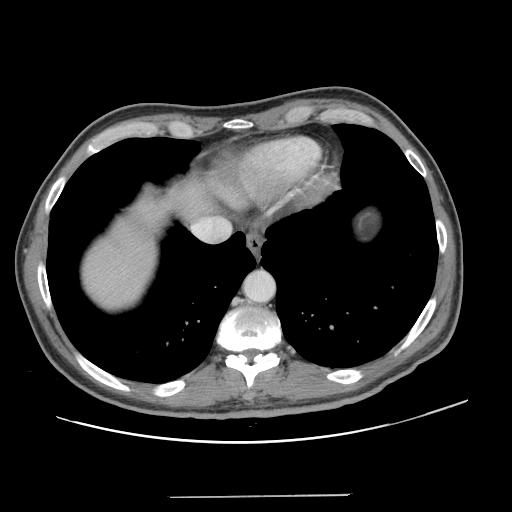
Contrast-enhanced abdominal CT, one axial slice. Slice 119 of 131 in the series (ordered by position). Intravenous contrast given. Soft-tissue window (W 400 / L 40 HU). 512 × 512 image matrix, field of view 403 × 403 mm. Male patient, age 60 years. From the clinical record (not read from this slice): diagnosis: colorectal cancer liver metastases, imaged before liver resection.
Structures marked on this image (outlined manually by an expert reader):
- liver: bounding box (x1, y1, x2, y2) in pixels: (82, 182, 211, 309)
- planned liver remnant (the part of the liver to remain after resection): (82, 208, 167, 309)